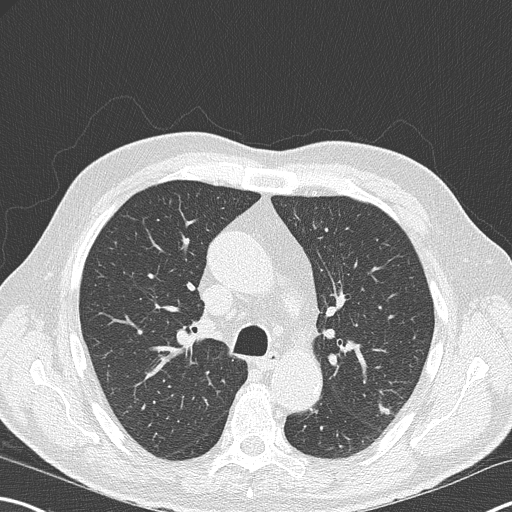
Chest CT (low-dose screening protocol), one axial image, second screening round (one year after baseline), lung window (W 1500 / L -600 HU), 2 mm slice thickness. Male, age 67 years at enrolment. Former smoker at enrolment.
Lesion marked by an expert reader, box from (x=371, y=393) to (x=411, y=429) px. Screening reader's record for this exam (one nodule recorded; not confirmed to be the boxed lesion): non-calcified nodule or mass ≥4 mm, left upper lobe, 9 × 6 mm, poorly defined margins, soft tissue attenuation, pre-existing on the prior screen: no. Later outcome: lung cancer diagnosed 418 days after this screen — squamous cell carcinoma, large cell, nonkeratinizing, NOS, left upper lobe, moderately differentiated (G2), stage IA (AJCC 6th edition), 15 mm at pathology.